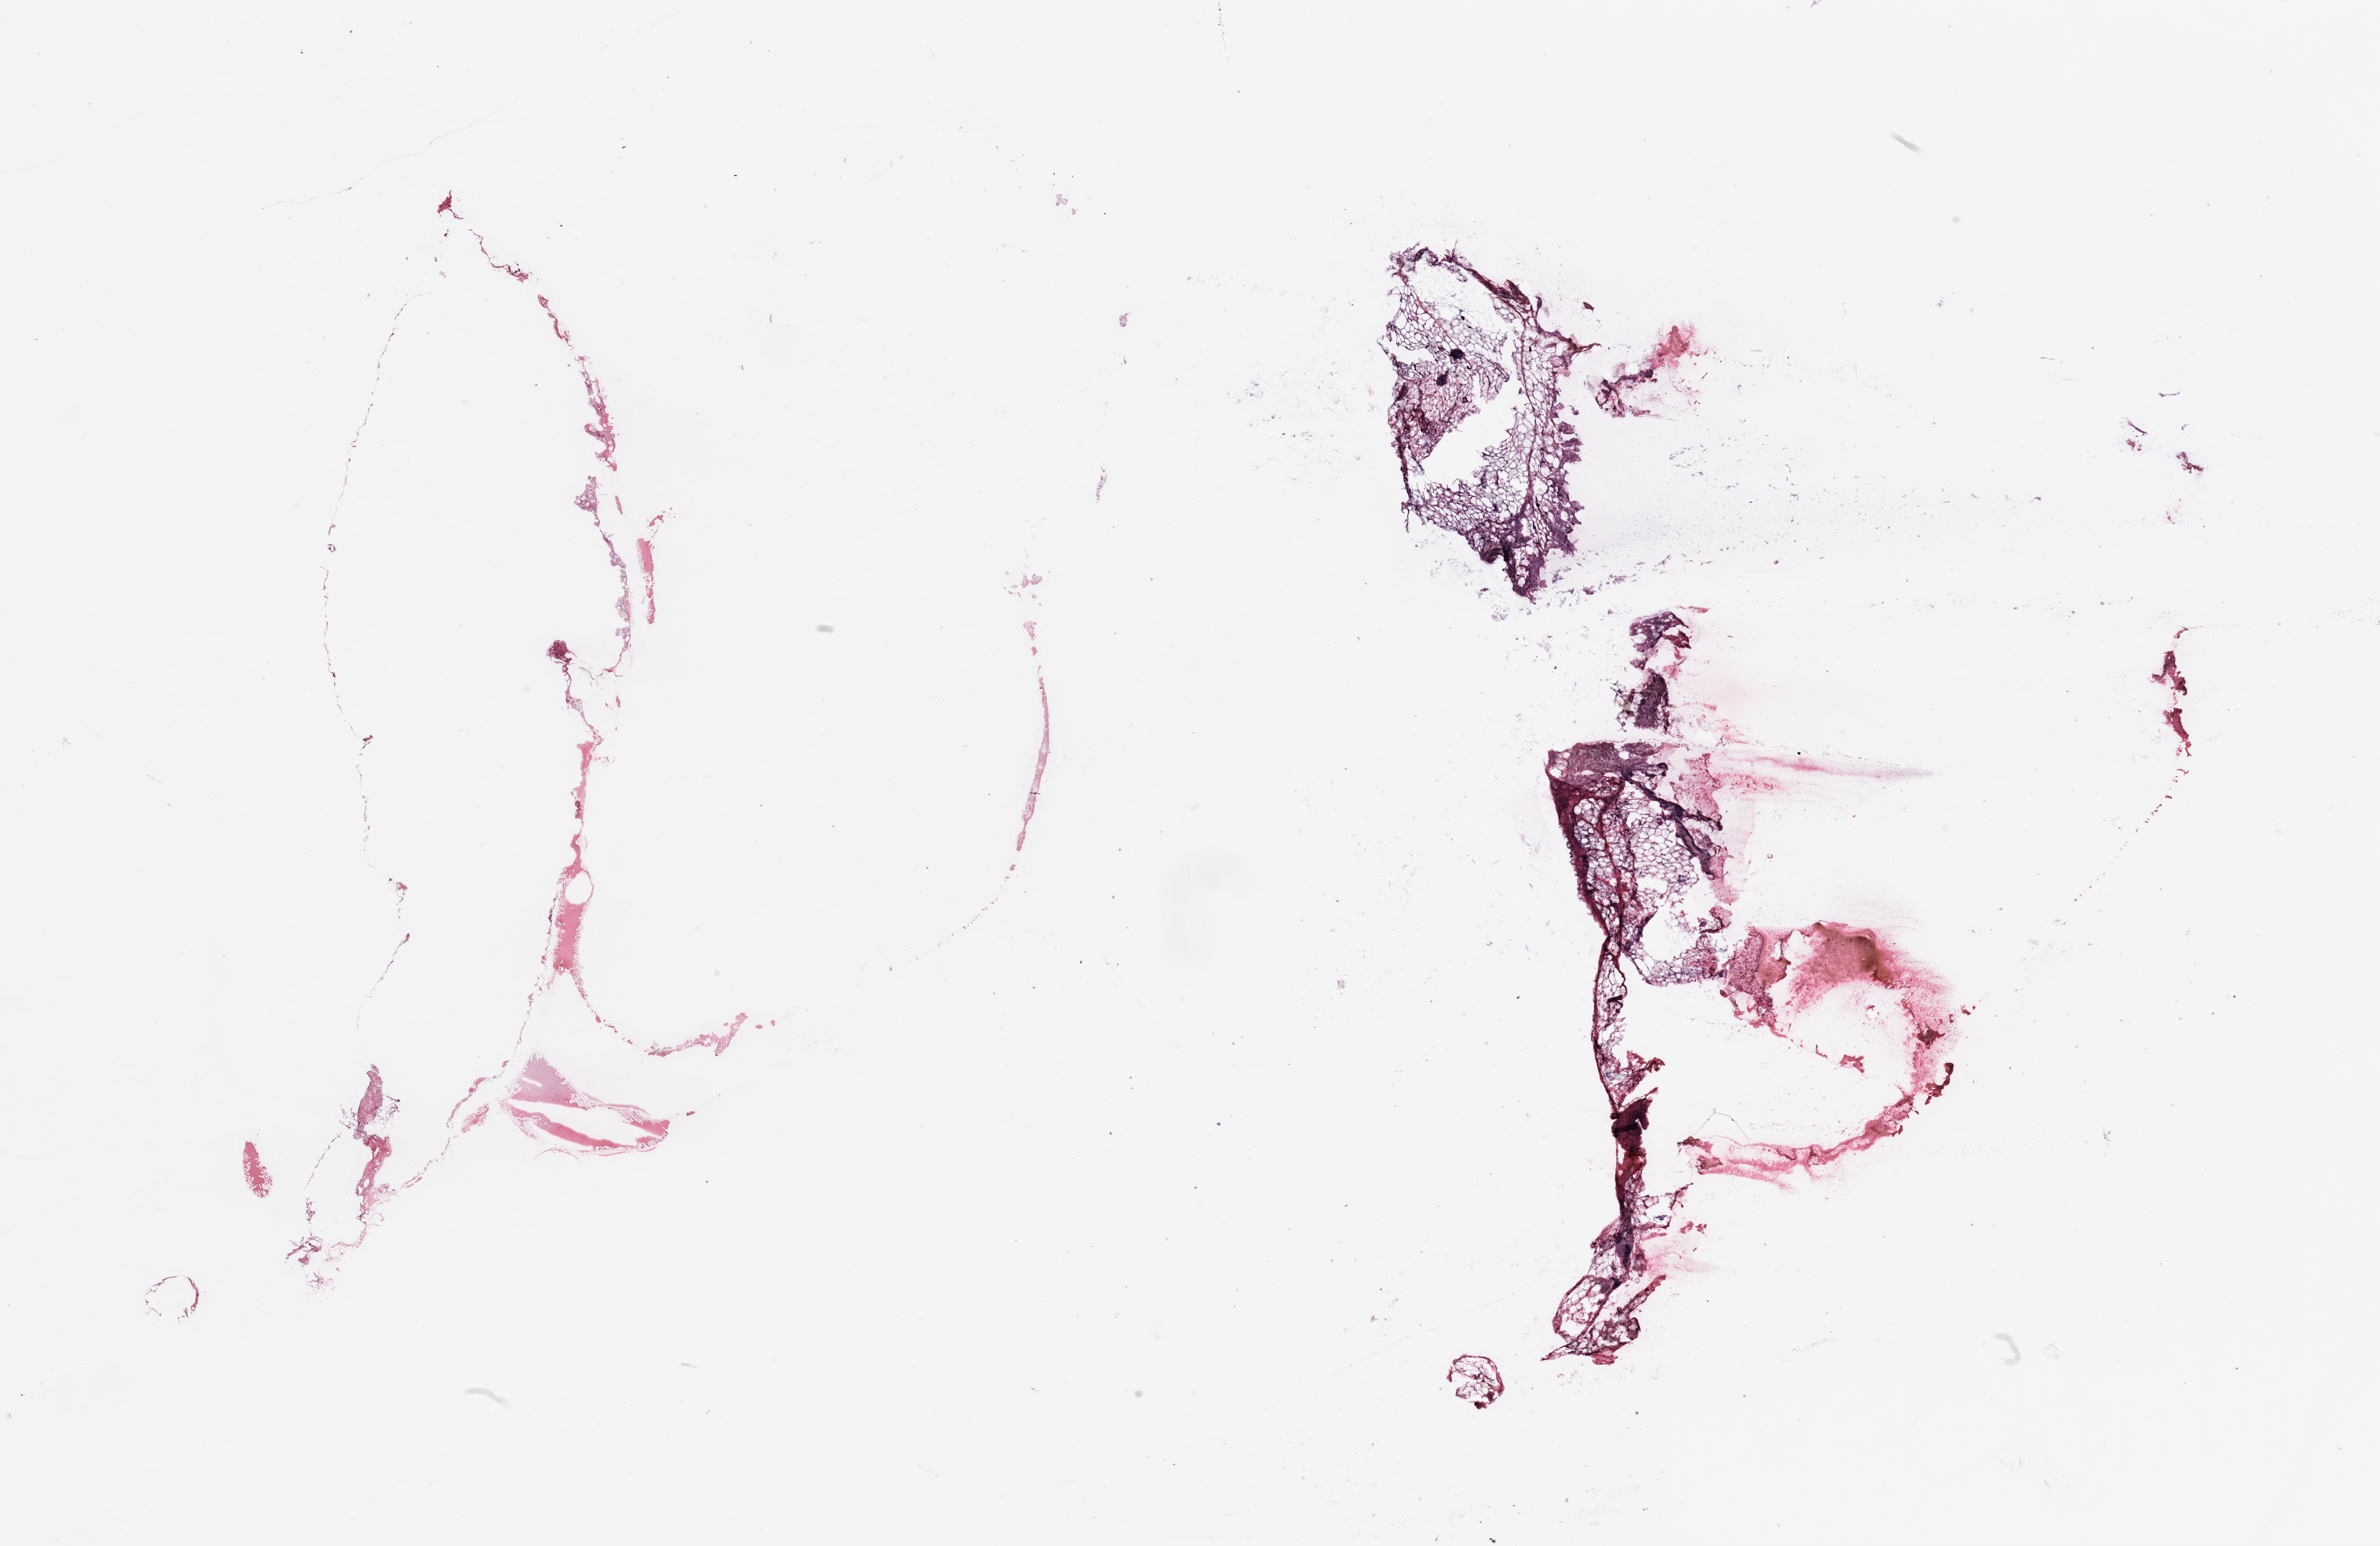
Digitized H&E tissue section (whole slide), a low-resolution overview of the entire scanned area, about 29.5 x 19.2 mm. Breast, tissue type not recorded. Female, 79 y/o.
Patient diagnosis: Infiltrating duct carcinoma, NOS.